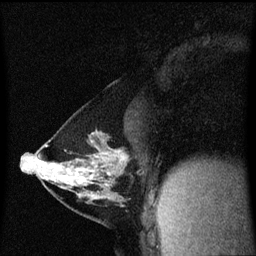
Breast MRI (dynamic contrast-enhanced), one sagittal slice; slice 31 of 60 in the series (ordered by position); dynamic contrast-enhanced series, image 2 of 3 at this slice position (ordered by acquisition); 1.5 T; TE 4.2 ms, TR 8.4 ms; 256 × 256 image matrix. Female patient, age 40 years. From the clinical record (not read from this slice): setting: breast cancer imaged before/during neoadjuvant chemotherapy; receptor status: triple-negative.
Structures marked on this image (semi-automatically segmented with operator editing):
- analysis volume of interest (the breast-tissue region the enhancement analysis was run in; not a lesion): bounding box <34,142,129,199> (left, top, right, bottom; pixels)
- tumour enhancement mask (voxels above the 70 % enhancement threshold inside the analysis volume of interest): <76,152,125,181>